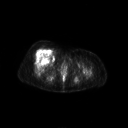
FDG PET of an extremity soft-tissue mass (from a PET/CT study), one axial slice. 128 × 128 image matrix, field of view 700 × 700 mm. Patient: female, 56 years. From the clinical record (not read from this slice): histological type: malignant solitary fibrous tumor; grade: intermediate; site of the primary tumour: right thigh.
Outlined on this slice (expert contour drawn on MRI and transferred to this co-registered scan by the dataset authors):
- gross tumour volume including surrounding oedema: bounding box (x1, y1, x2, y2) in pixels: (34, 48, 53, 62)
- gross tumour volume (mass): (34, 49, 52, 62)